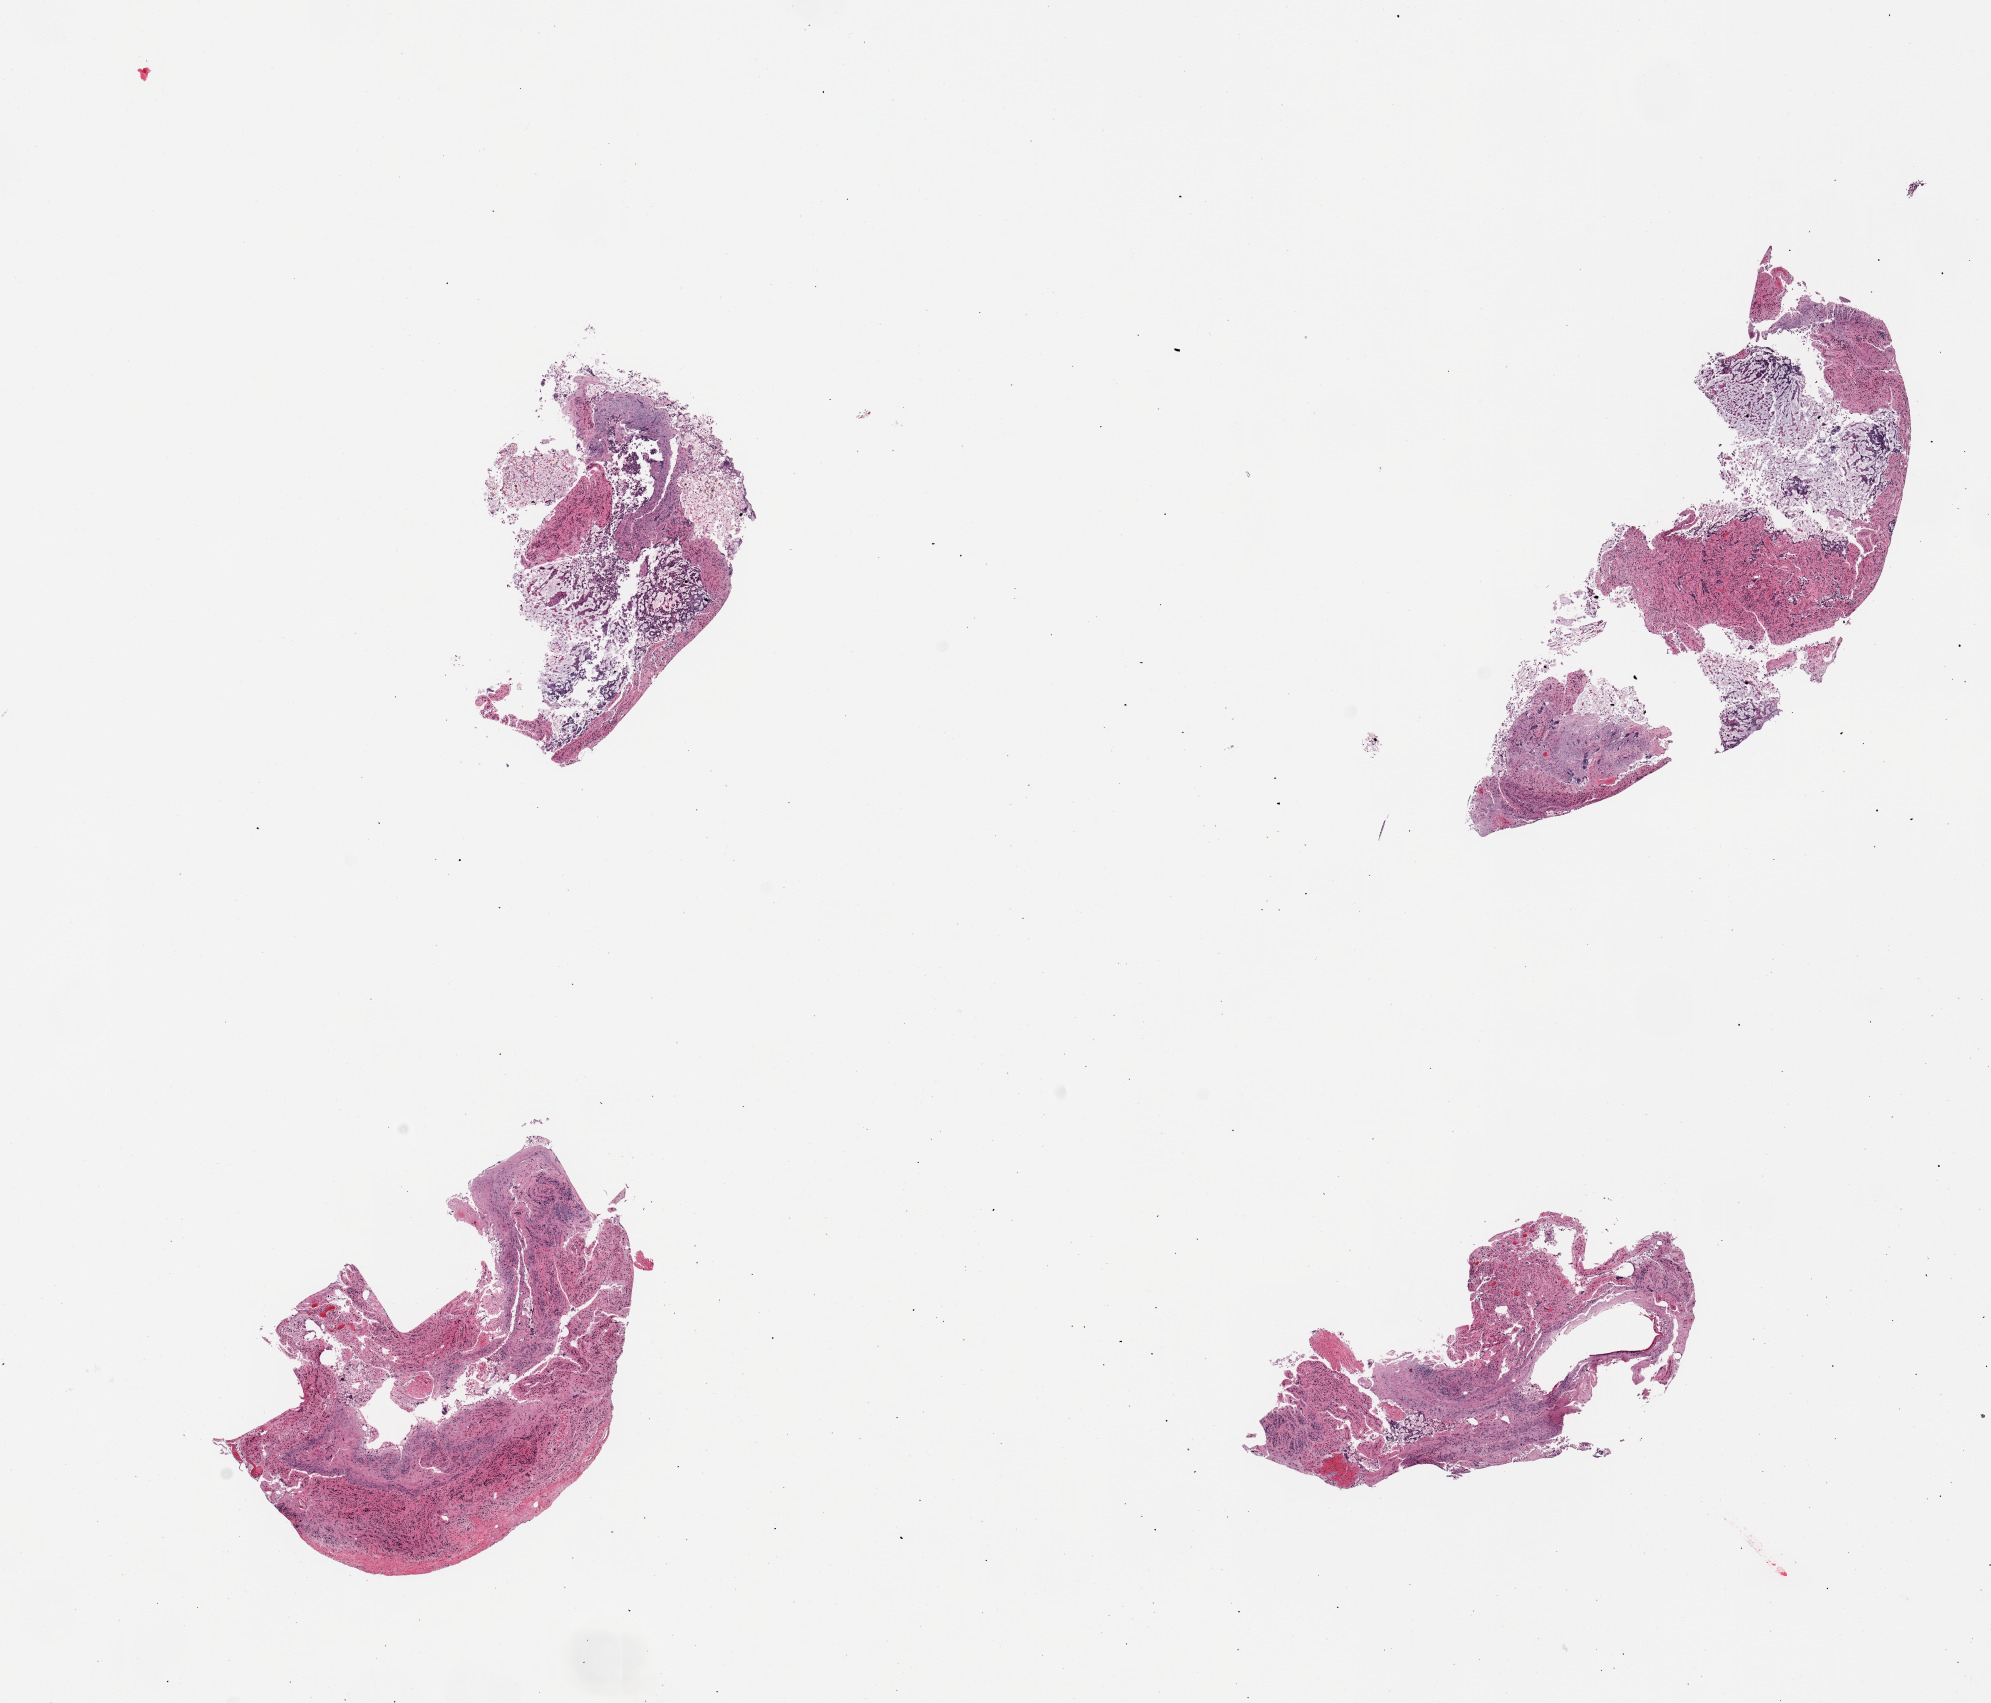
H&E whole-slide image — whole scanned area (about 15.8 x 13.5 mm, from a 20x scan) shown as a low-resolution overview. PAXgene-fixed, paraffin-embedded tissue. Target tissue: ileum. Tissue donor sample.
Reviewer comment on this tissue sample: 4 pieces; total autolysis.